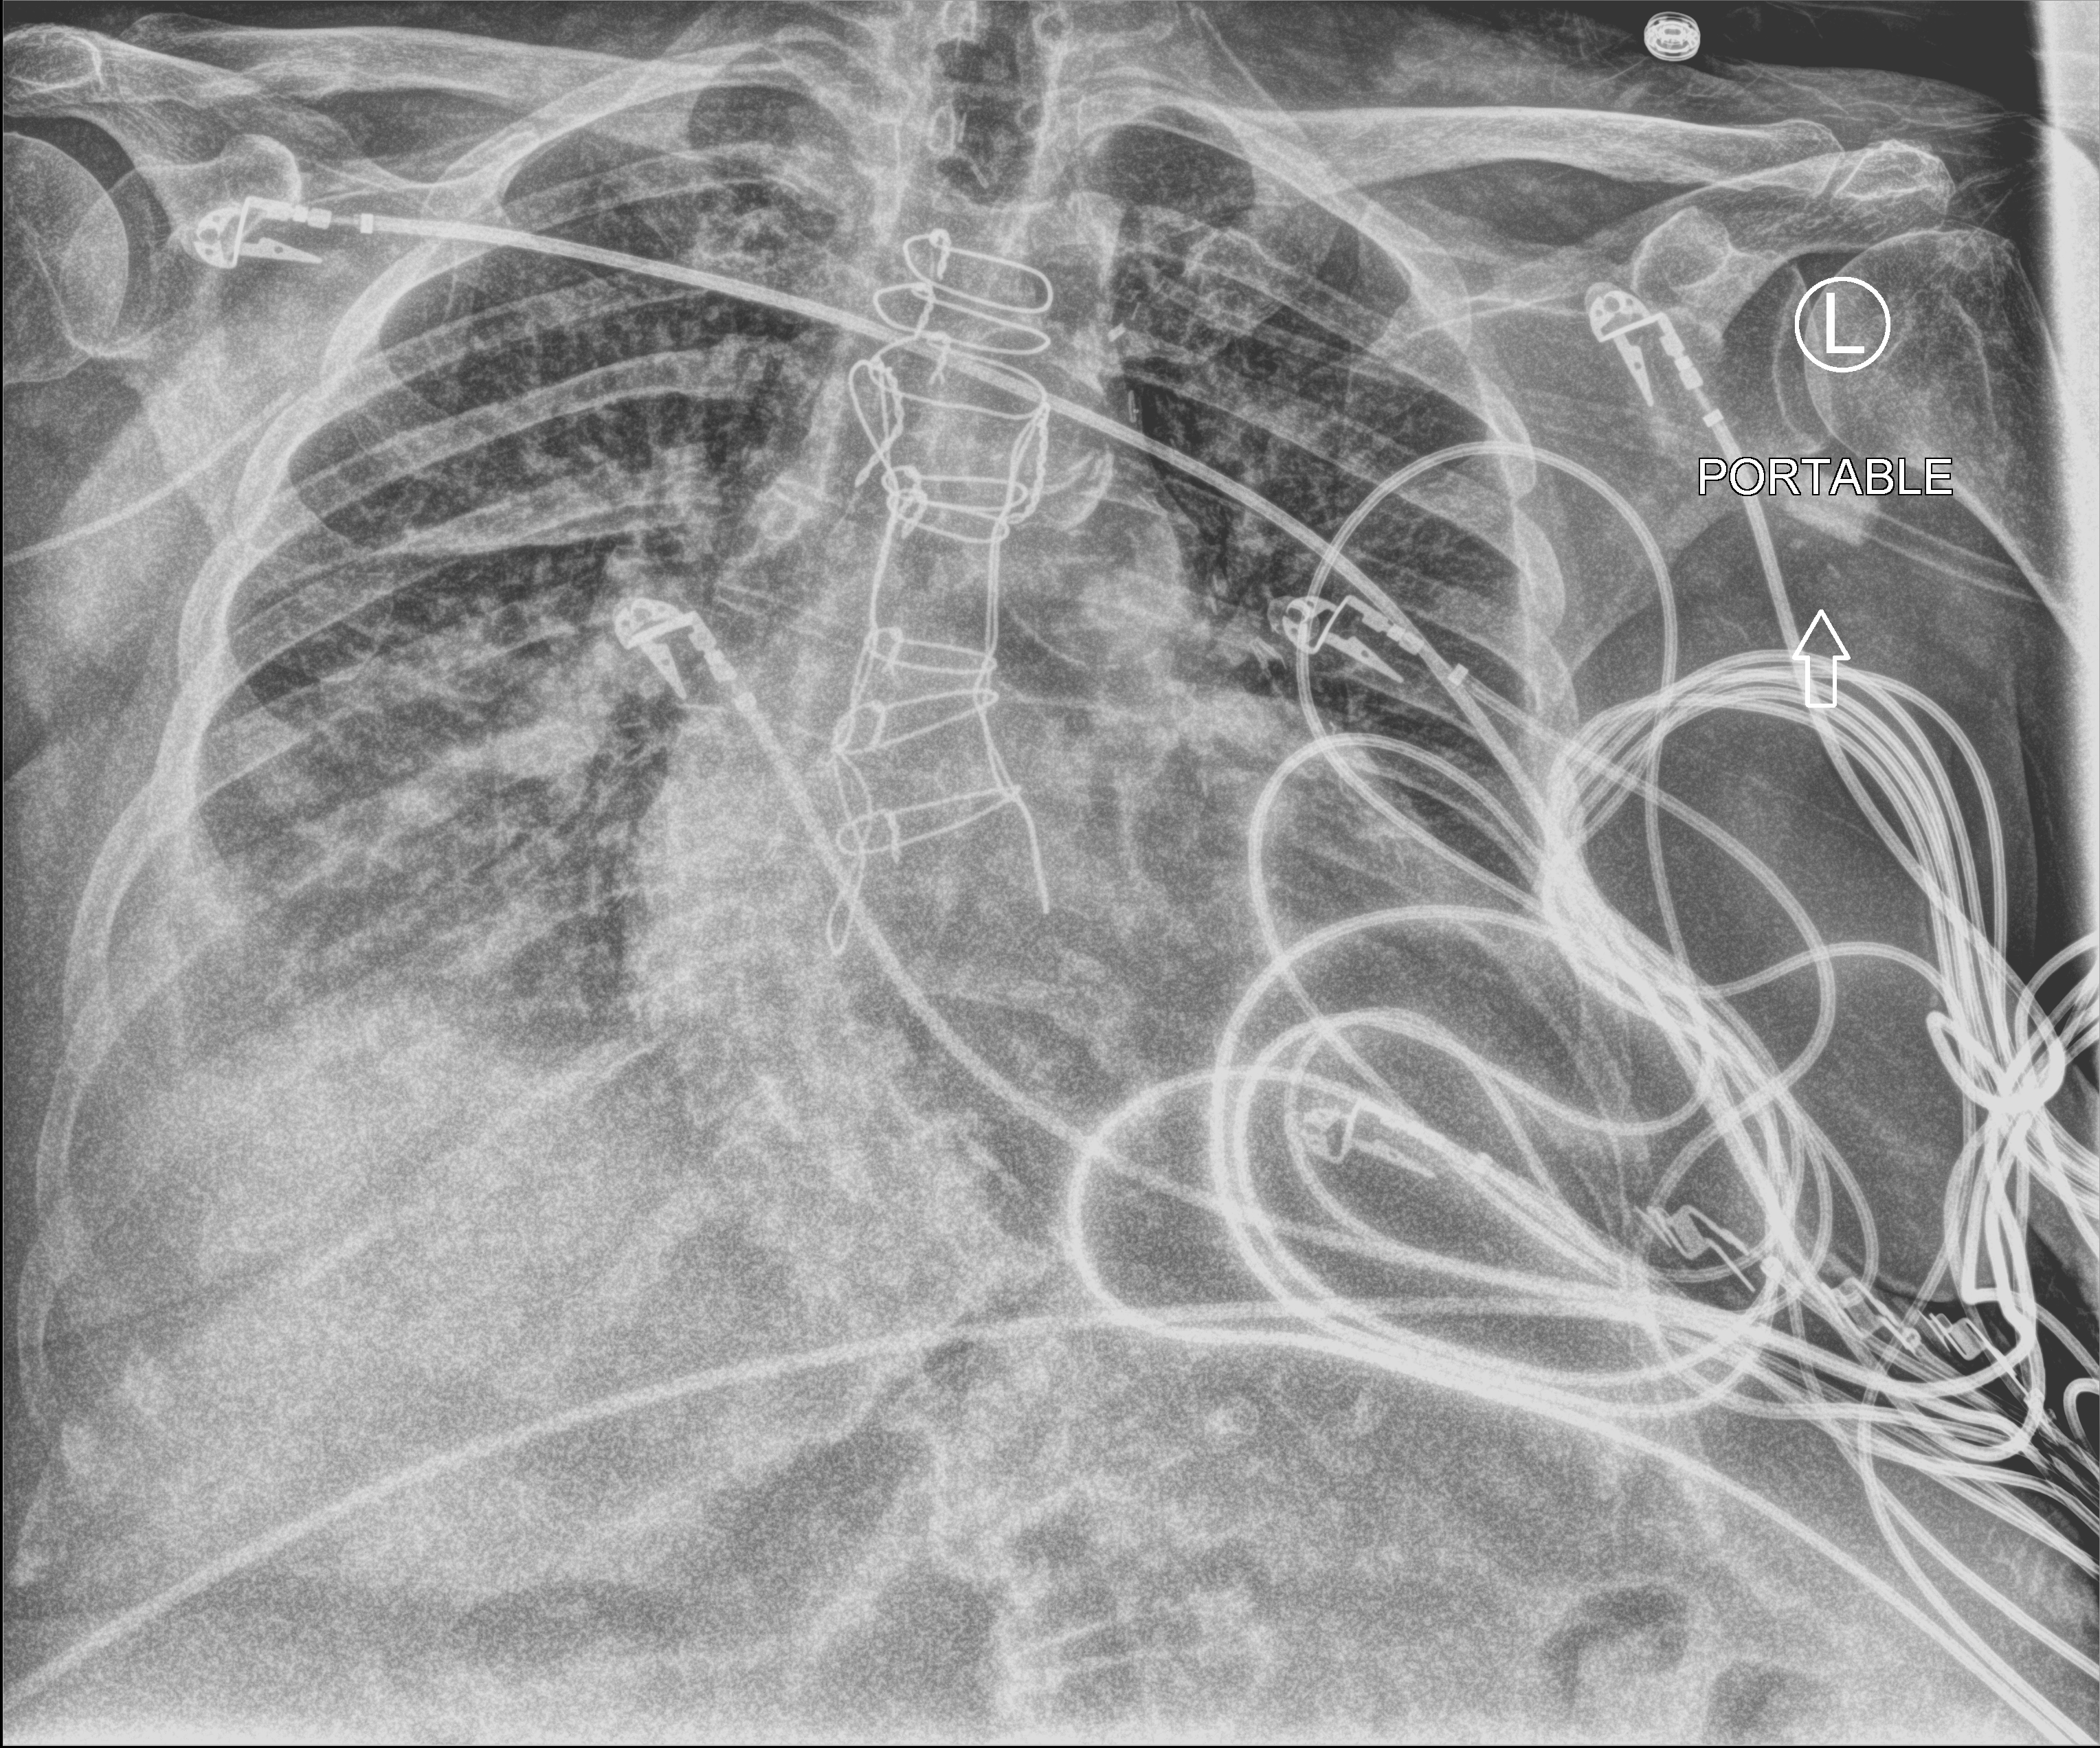
Chest X-ray (portable), anteroposterior (AP) projection. Patient hospitalised with COVID-19; female, aged 75–90 years.
Hospital-stay facts (about this admission, not read from this image; timing relative to this image not recorded):
- admitted to intensive care during this hospital stay: no